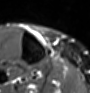
MRI of an extremity soft-tissue mass, one axial slice. Slice 13 of 60 in the series (ordered by position). STIR. MR volume resampled by the dataset authors to the PET/CT grid (not the native acquisition matrix). 3.27 mm slice thickness. 90 × 93 image matrix. Female patient. From the clinical record (not read from this slice): histological type: undifferentiated – high grade; grade: high; site of the primary tumour: right thigh.
Annotated regions visible in this slice (expert contour drawn on MRI and transferred to this co-registered scan by the dataset authors):
- gross tumour volume (mass): bounding box [x1, y1, x2, y2] px = [42, 40, 45, 43]